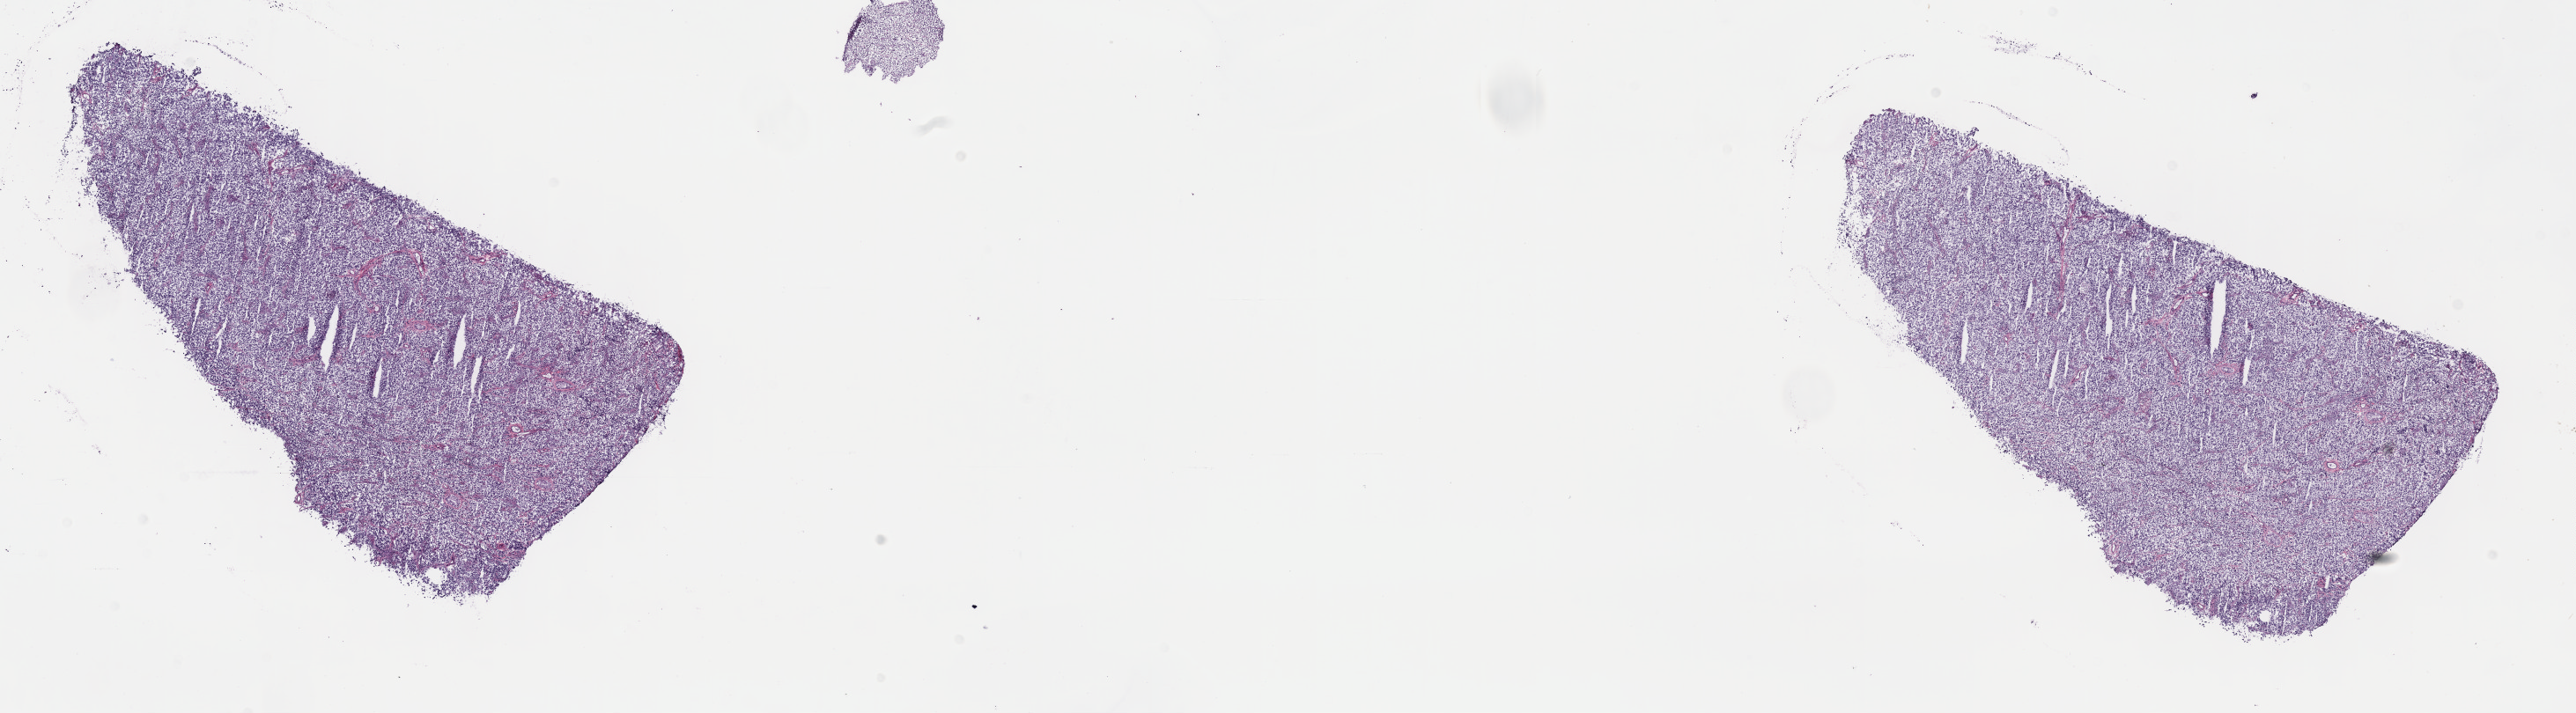
H&E-stained whole-slide image — whole scanned area (about 23.7 x 6.6 mm, acquisition: 40x scan) shown as a low-resolution overview; frozen section from the top of the tissue portion; sample: primary tumour, testis. Patient: male, age at initial diagnosis 28 years. Pathologist review of this section (percent, as recorded): tumour cells 90%, tumour nuclei 90%, normal cells 0%, stromal cells 10%, necrosis 0%. Infiltration values recorded for this section: lymphocyte infiltration 60%, monocyte infiltration 20%, neutrophil infiltration 10%.
Histologic diagnosis: Seminoma, NOS. TNM: T1 N0 M0. AJCC pathologic stage: IS (6th edition).